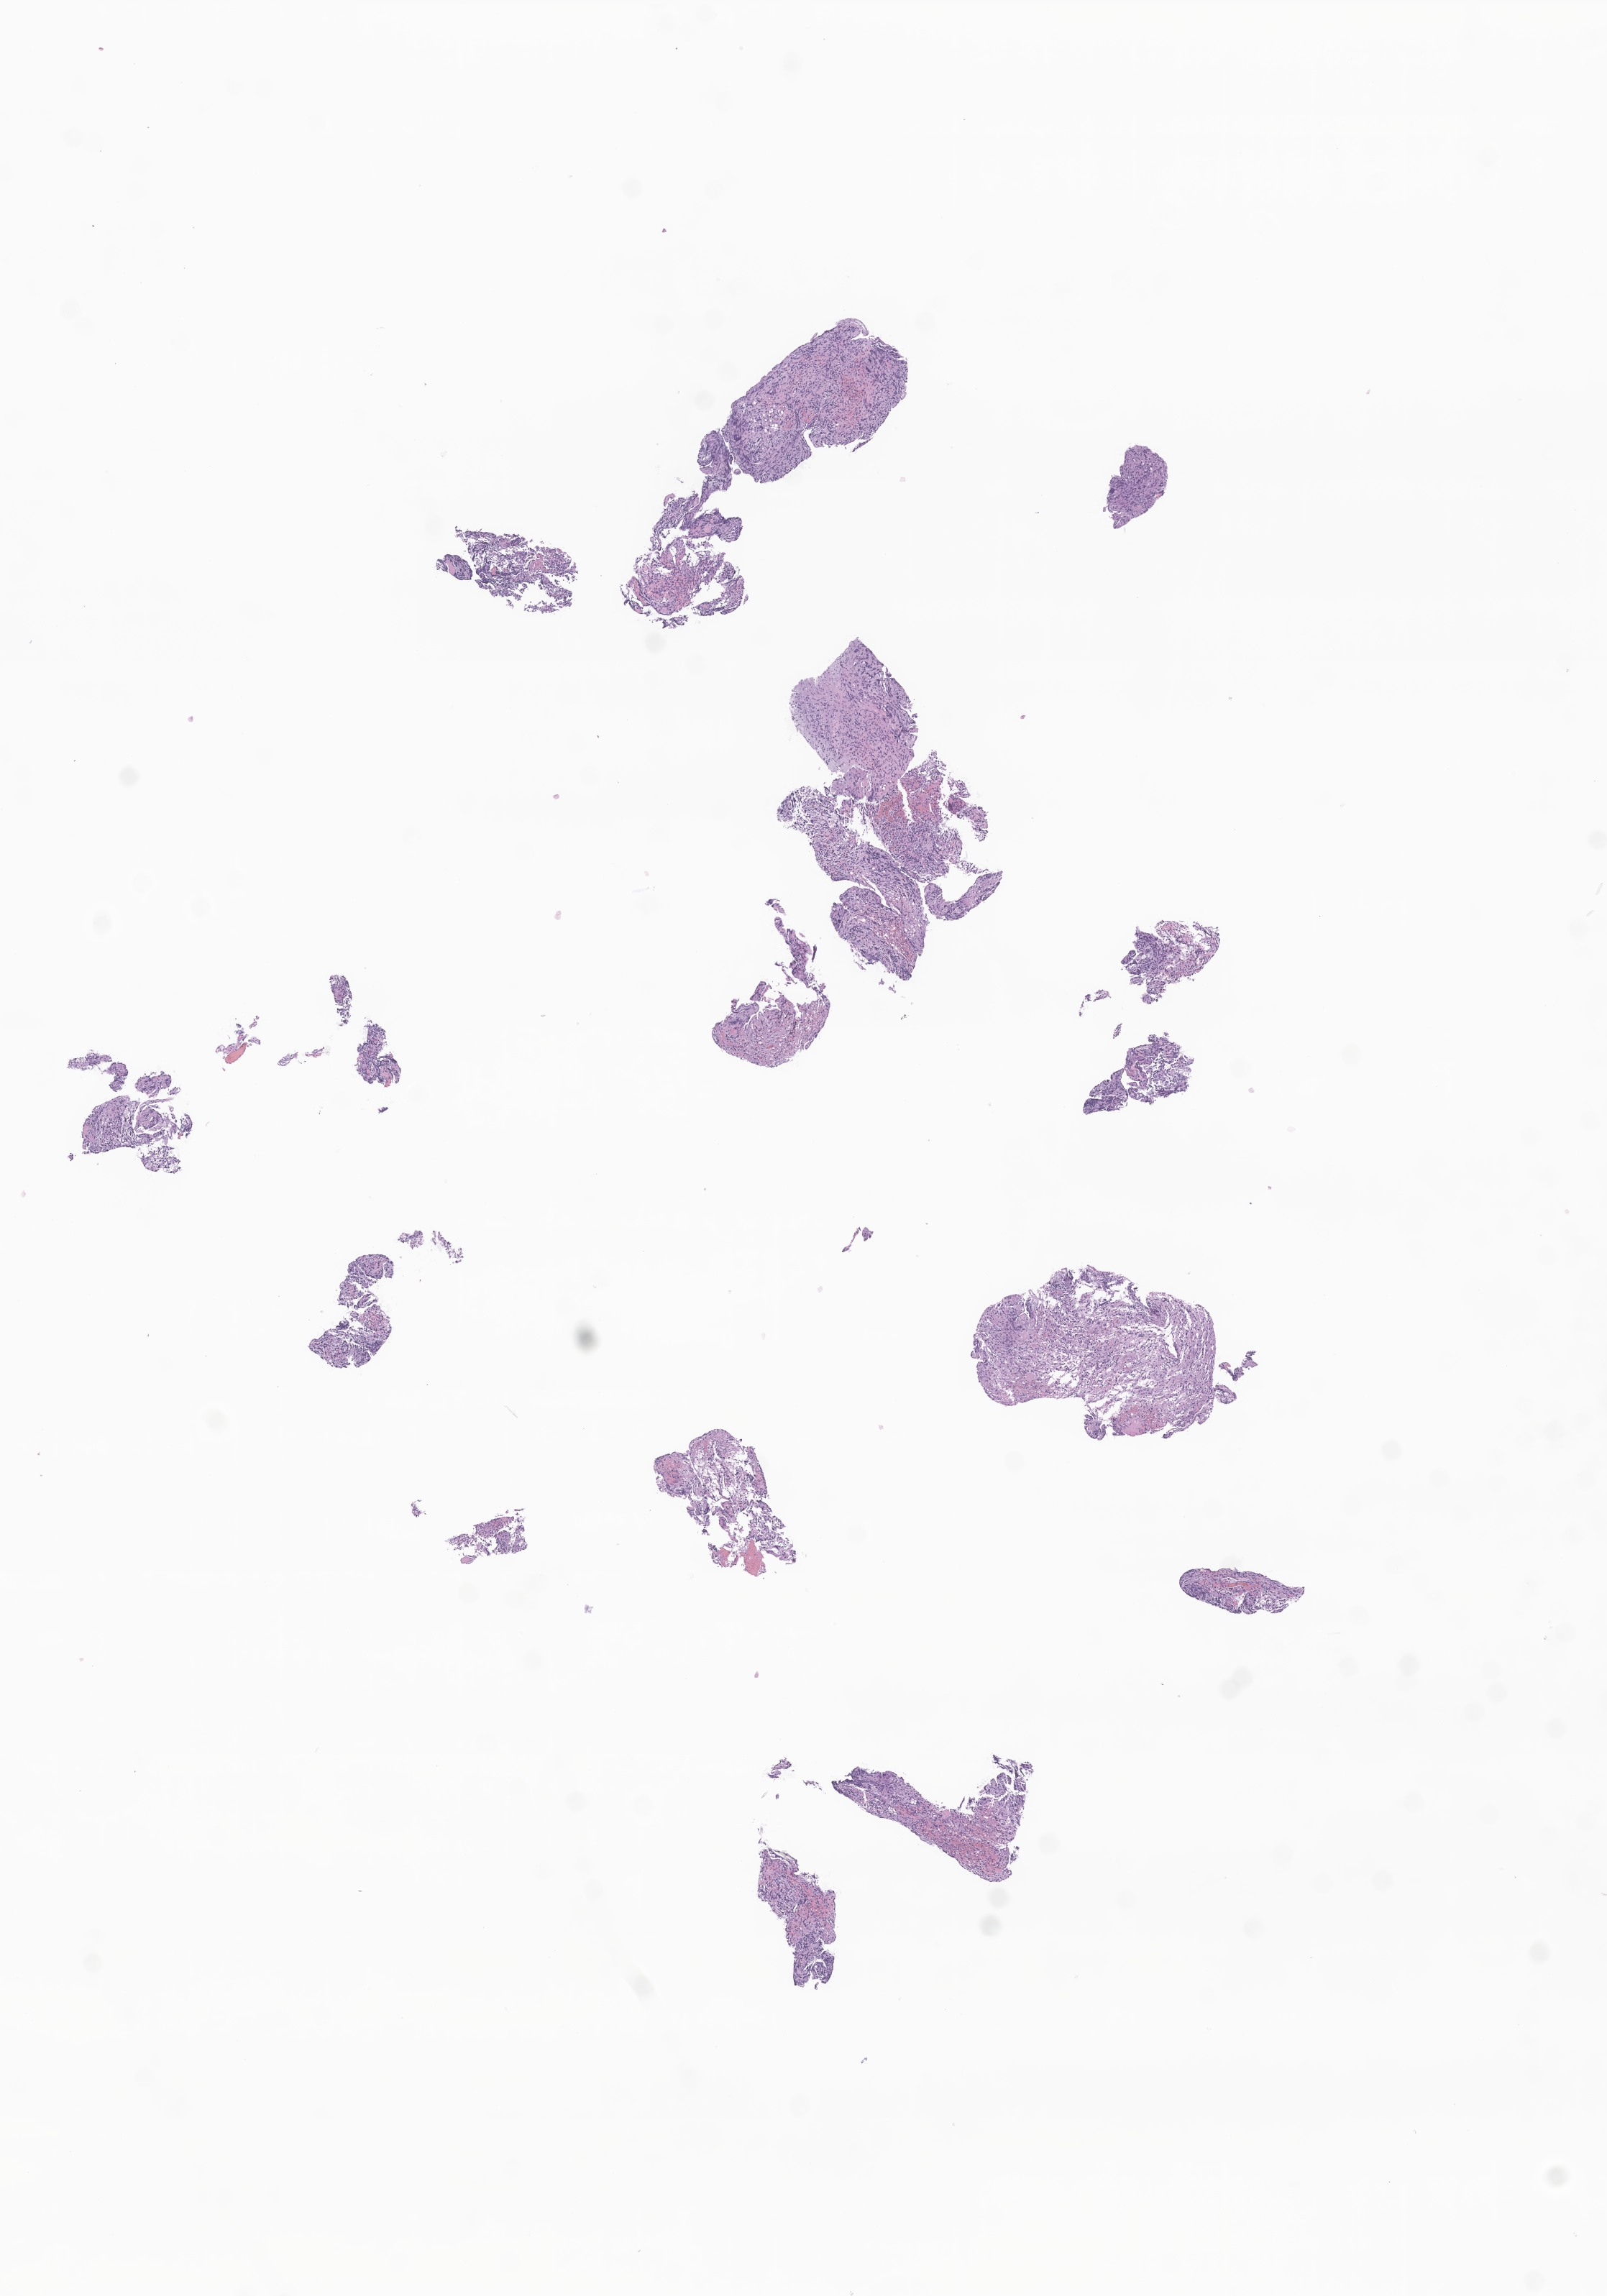
Haematoxylin and eosin whole-slide image of tumor tissue from the brain, shown as a low-resolution overview of the whole scanned area (about 9.4 x 13.5 mm), formalin-fixed paraffin-embedded section. Patient female; age 196 months (16 years 4 months).
Diagnosis: Glioma, malignant.